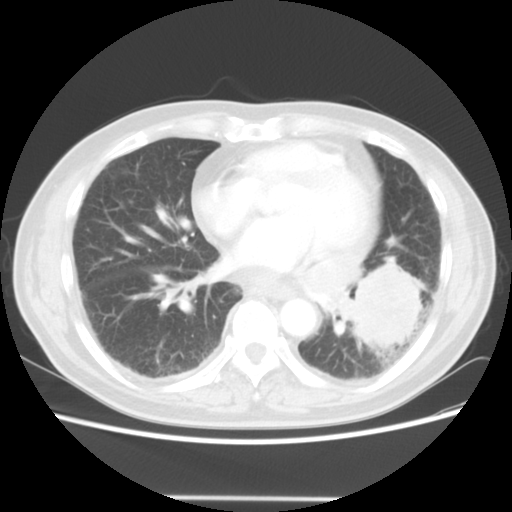
Chest CT, one axial slice. Slice 20 of 56 in the series (ordered by position). 140 kVp. Lung window (W 1500 / L -600 HU). 5 mm slice thickness. 512 × 512 image matrix, field of view 360 × 360 mm. Patient: male, 66 years. From the clinical record (not read from this slice): clinical TNM (as recorded): T4 N3 M0; histopathological grade: G3.
Outlined on this slice (bounding box drawn by a radiologist):
- lung tumour (recorded histology: small cell carcinoma): bounding box [x1, y1, x2, y2] px = [348, 262, 425, 352]